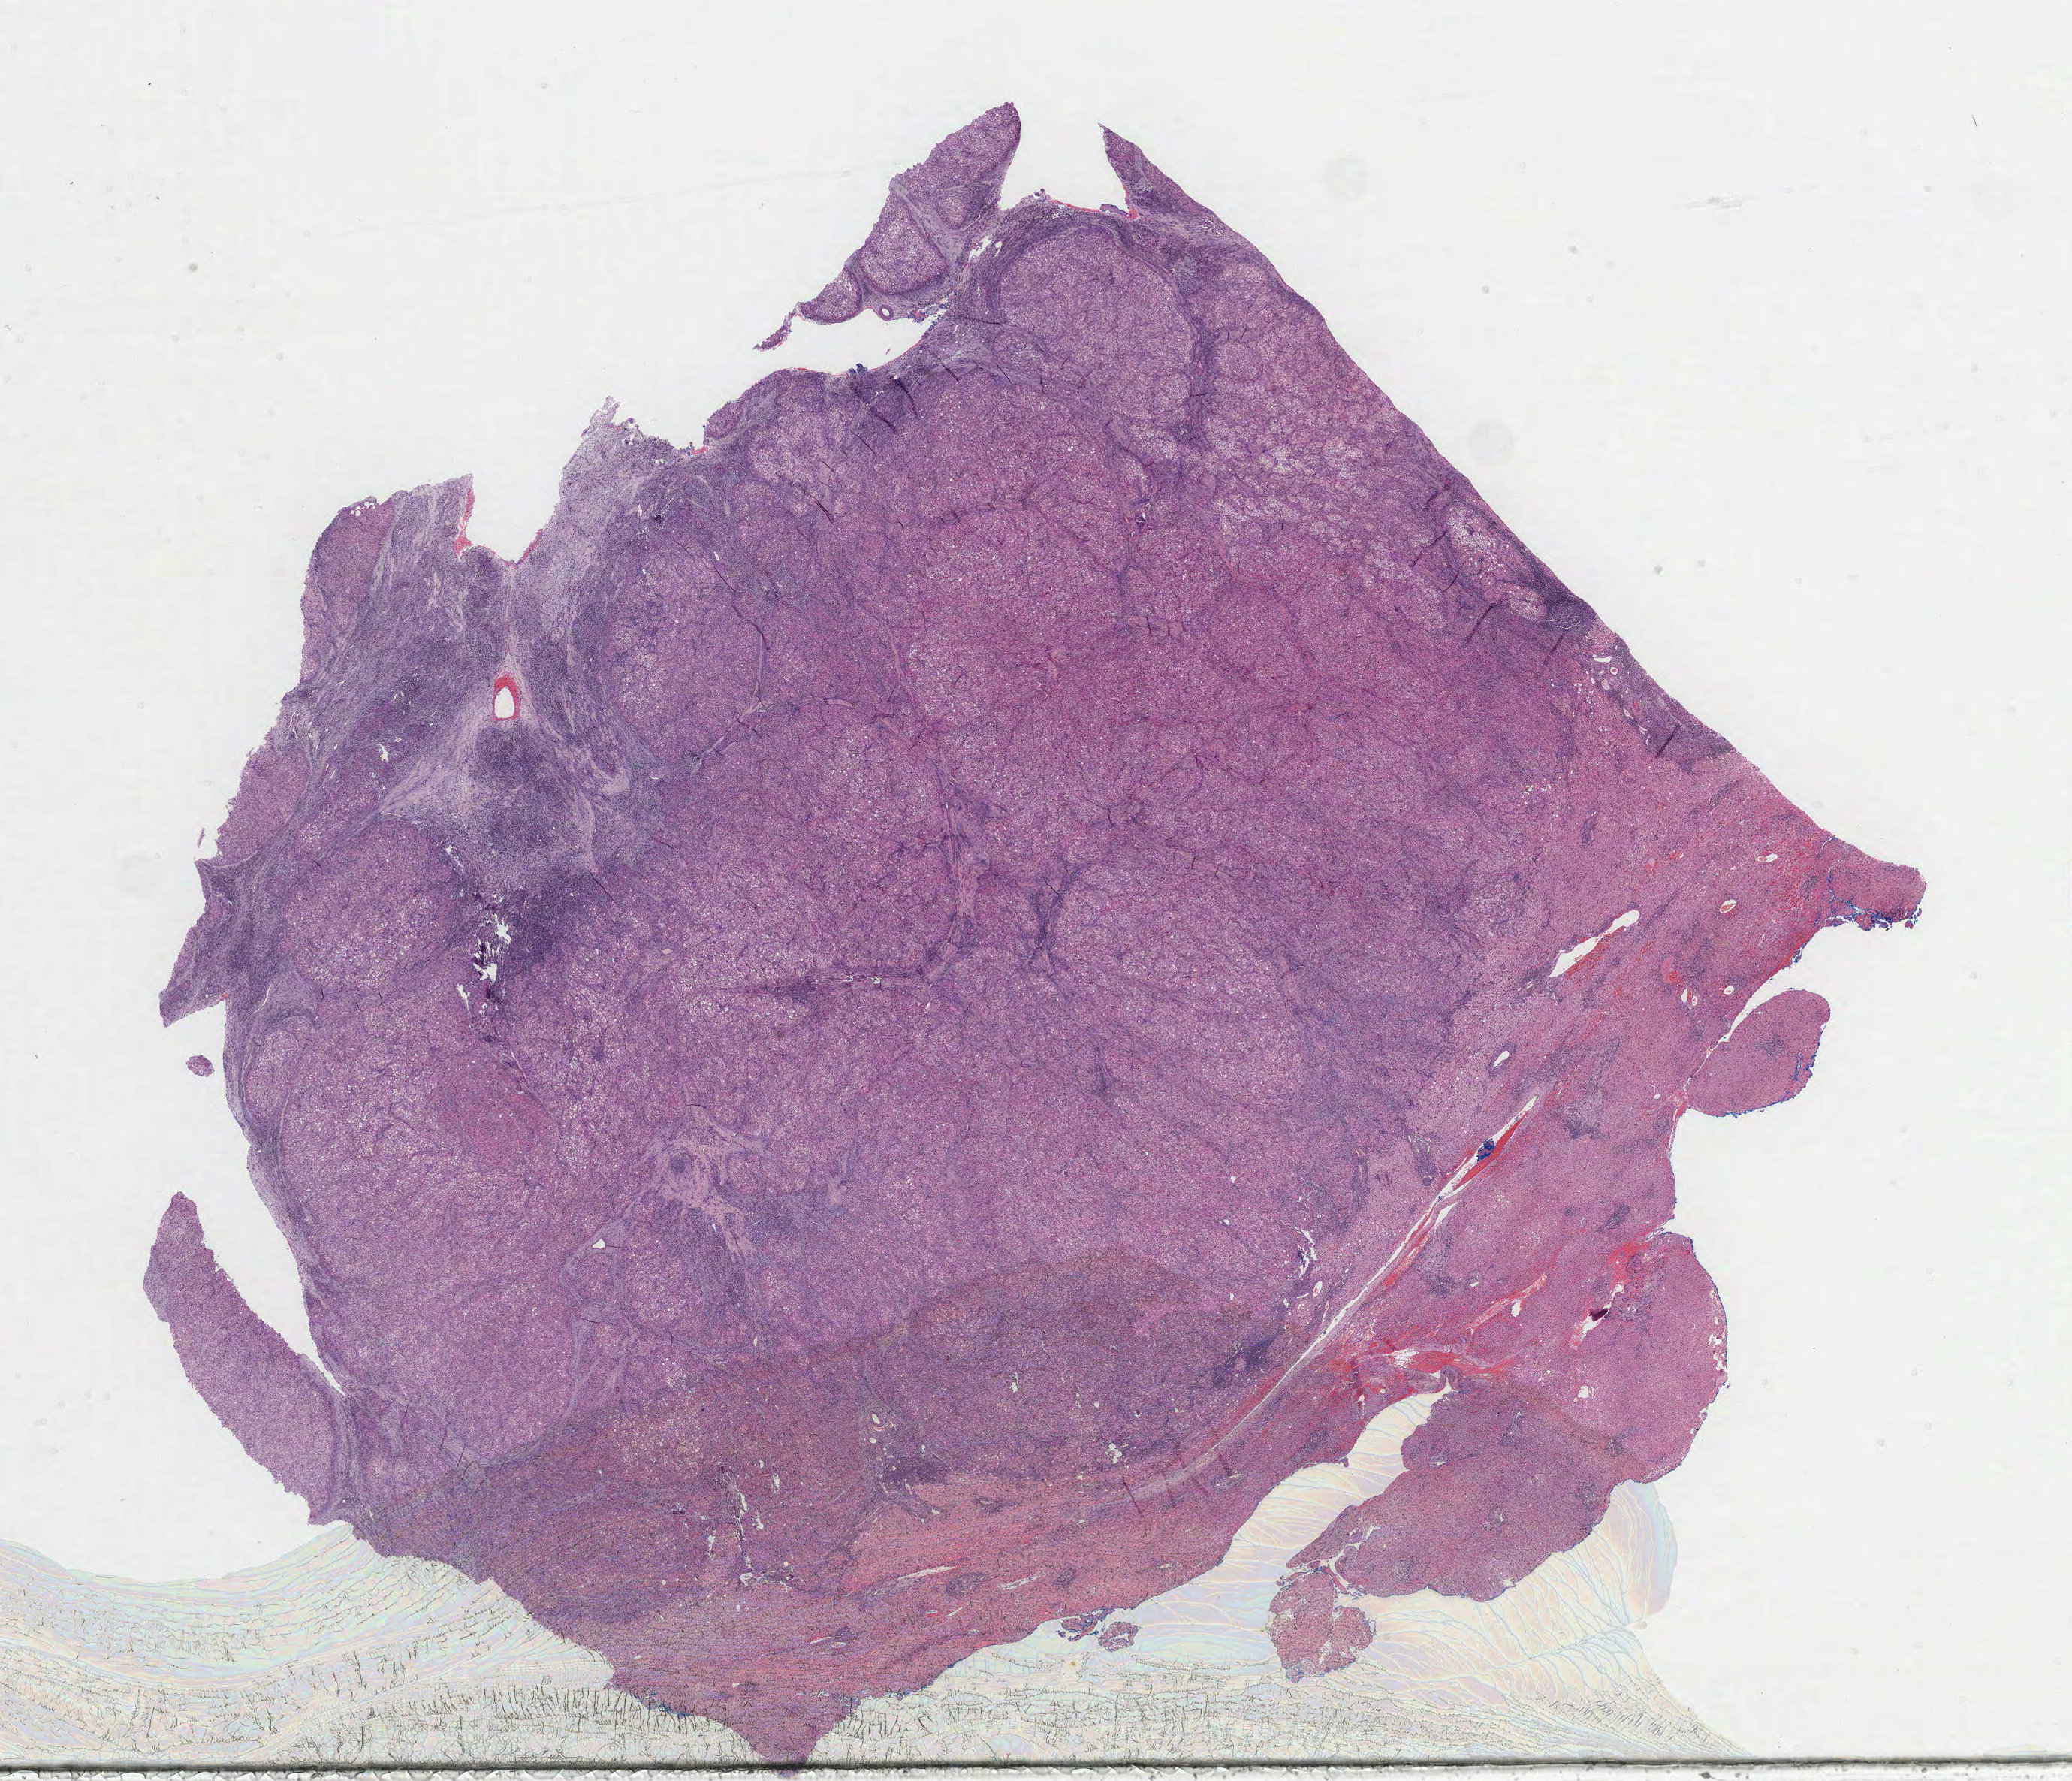
Digitized Hematoxylin and eosin (H&E) stained tissue section (whole slide), shown as a low-resolution overview of the whole scanned area (about 22.3 x 19.2 mm); formalin-fixed paraffin-embedded (FFPE) diagnostic section; primary tumour sample from the liver. Male patient; age at initial diagnosis 68 years. Histologic grade: G2 (moderately differentiated).
AJCC pathologic stage: I (6th edition). Diagnosis: Hepatocellular carcinoma, NOS.